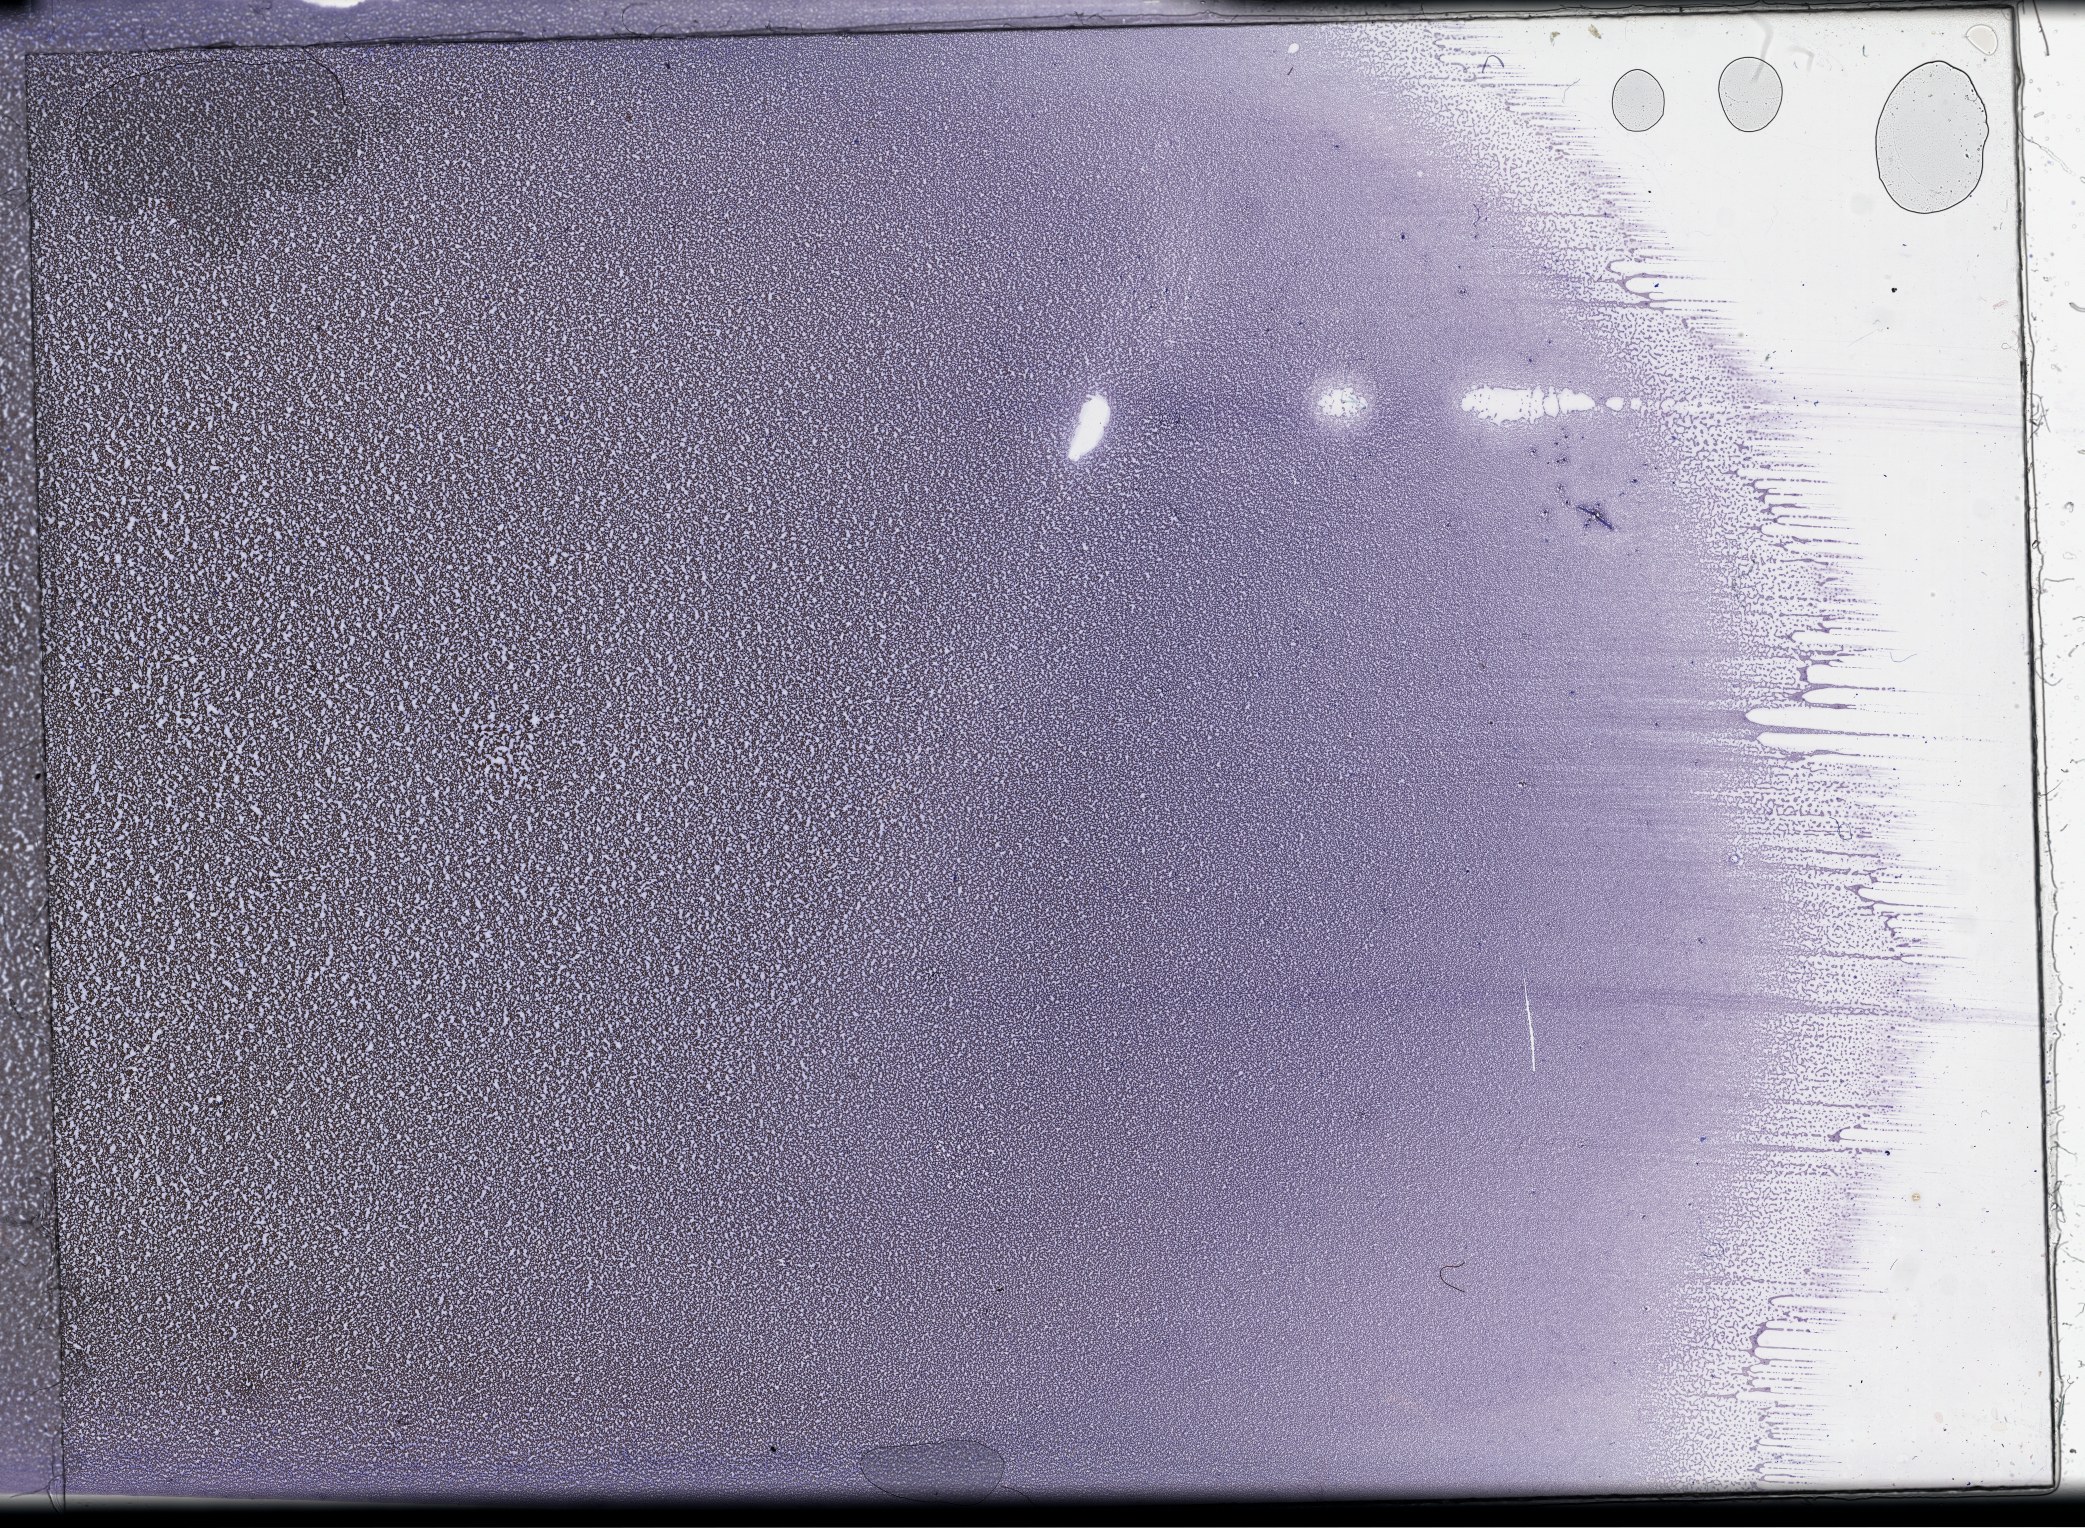
Digitized H&E-stained tissue section (whole slide), whole scanned area (about 33.7 x 24.7 mm, from a 40x scan) shown as a low-resolution overview. Peripheral blood (leukaemic) sample. 76-year-old female patient.
- FAB classification: M4
- diagnosis: Acute Myeloid Leukemia